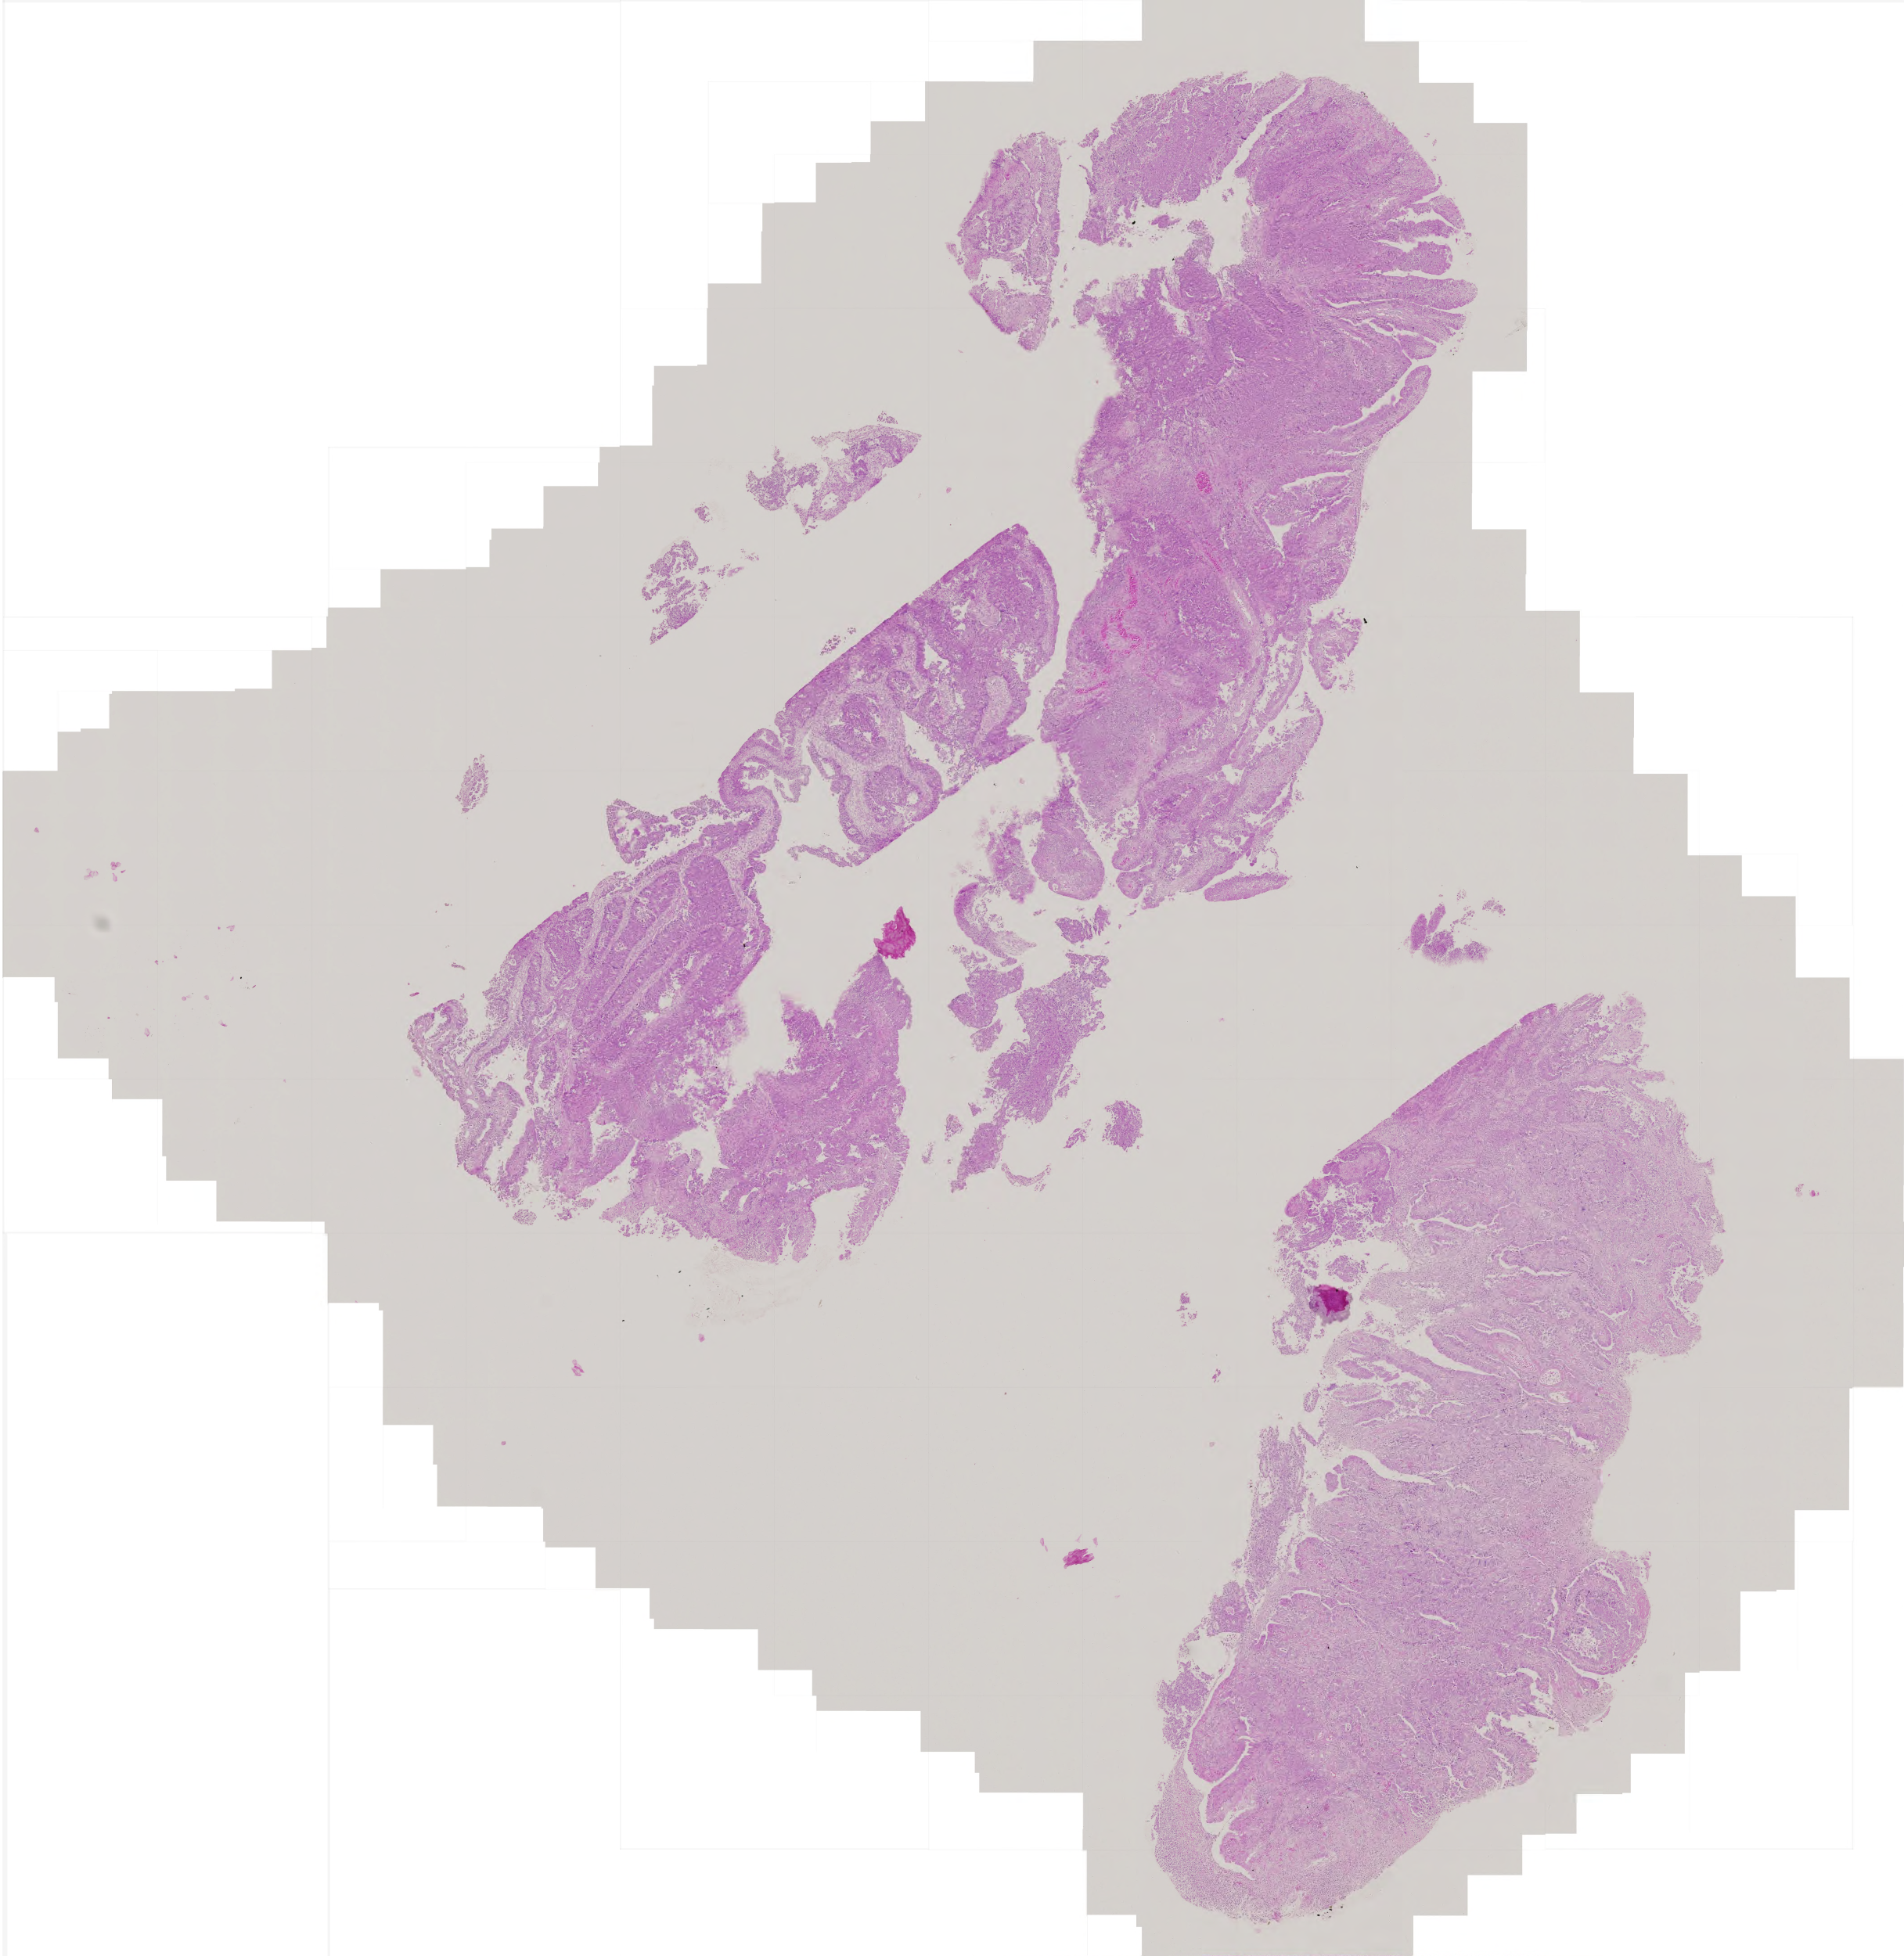
Whole-slide histology image, H&E, shown as a low-resolution overview of the whole scanned area (about 4.9 x 5.0 mm). FFPE section. Primary tumour sample from the colon. Patient: female, age at initial diagnosis 83 years.
Diagnosis: Adenocarcinoma, NOS (ascending colon).